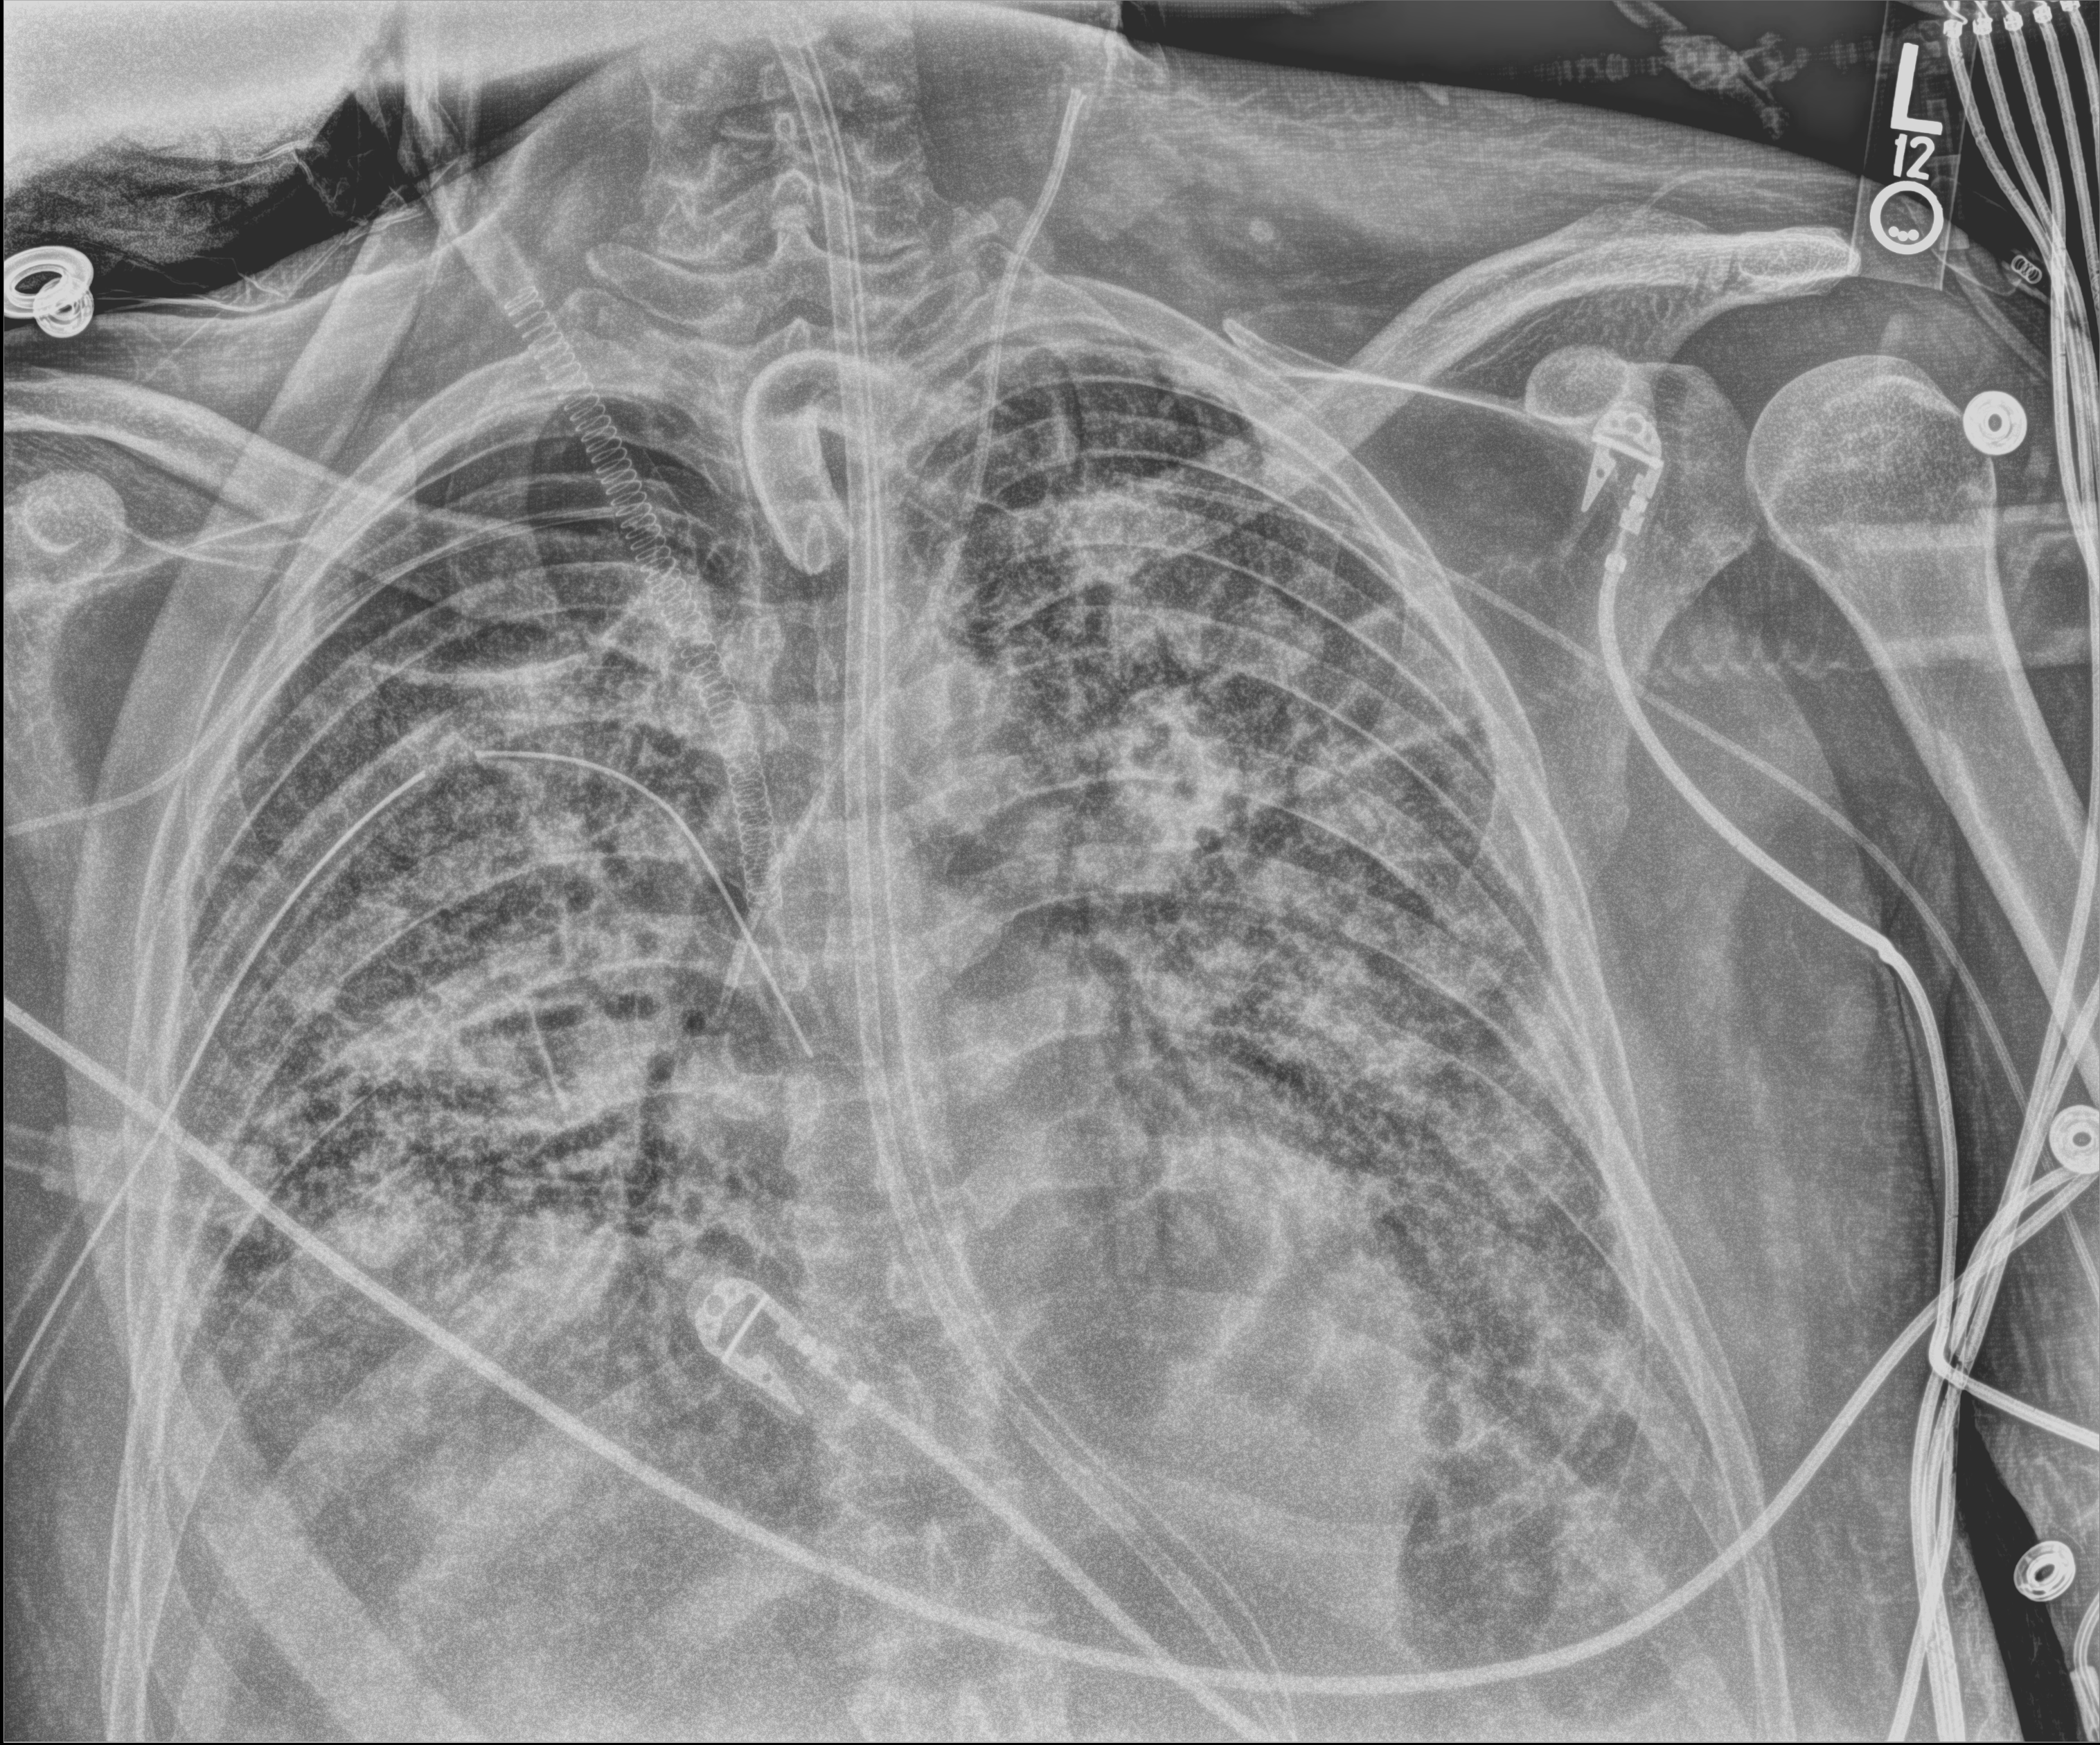
Chest radiograph (digital radiography). Adult patient hospitalised with COVID-19, age 18–59 years.
From the hospital-stay record, not from the radiograph (when in the stay this image was taken is not recorded): length of hospital stay: 60 days; admitted to intensive care during this hospital stay: yes; mechanically ventilated during this hospital stay: yes.